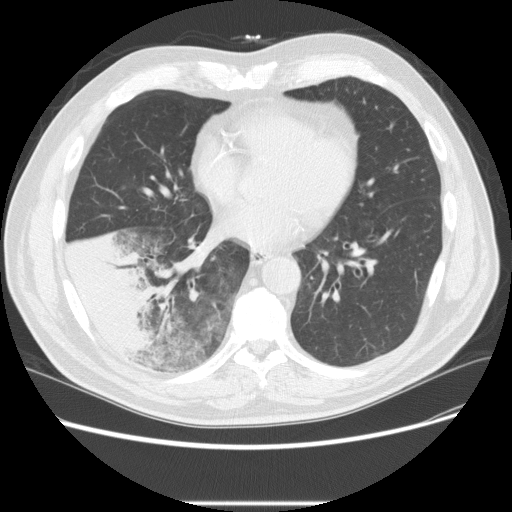
Low-dose screening chest CT, one axial slice; reconstruction kernel STANDARD; 120 kVp; lung window (W 1500 / L -600 HU); 2.5 mm slice thickness; 512 × 512 image matrix, field of view 380 × 380 mm.
Structures marked on this image (outlined manually by an expert reader):
- lesion 3 (tumor, lower lobe of right lung): bounding box [x1, y1, x2, y2] px = [69, 231, 158, 355]